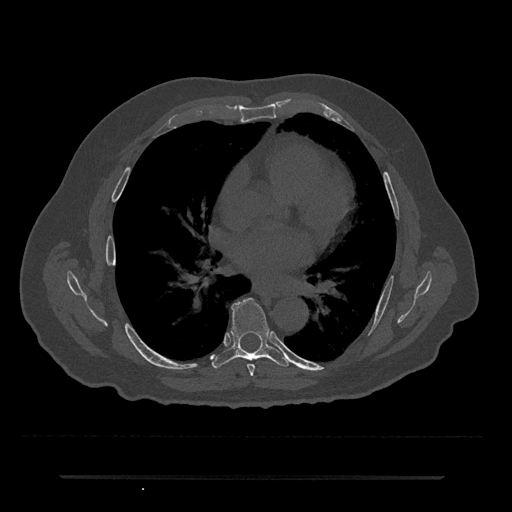
CT including the spine, one axial slice; slice 399 of 797 in the series (ordered by position); reconstruction kernel Br40s/3; bone window (W 1800 / L 400 HU); 512 × 512 image matrix. Male patient, age 69 years. Case-level facts recorded for this patient, not image findings: primary cancer: prostate.
Annotated regions visible in this slice (semi-automatic segmentation, software-assisted and operator-edited):
- T6 vertebra: bounding box (x1, y1, x2, y2) in pixels: (247, 364, 255, 376)
- T7 vertebra: (212, 298, 289, 369)